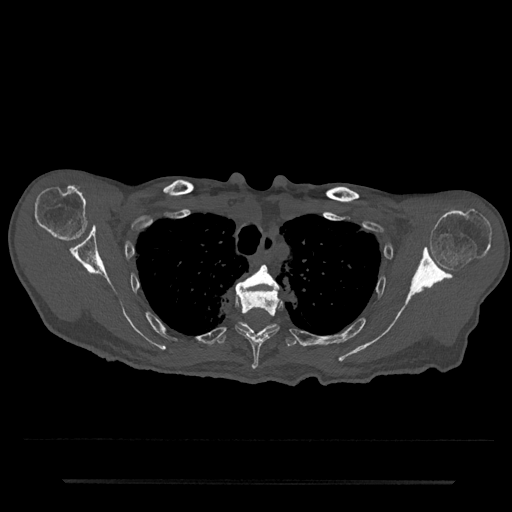
CT including the spine, one axial slice; slice 617 of 797 in the series (ordered by position); reconstruction kernel Br40s/3; bone window (W 1800 / L 400 HU); 0.5 mm slice thickness; 512 × 512 image matrix, field of view 427 × 427 mm. Patient: male, 74 years. From the clinical record (not read from this slice): primary cancer: prostate.
Structures marked on this image (semi-automatic segmentation, software-assisted and operator-edited):
- T3 vertebra: box from (x=236, y=265) to (x=280, y=292) px
- T4 vertebra: (x=236, y=287)–(x=282, y=370)
- T5 vertebra: (x=216, y=322)–(x=297, y=347)